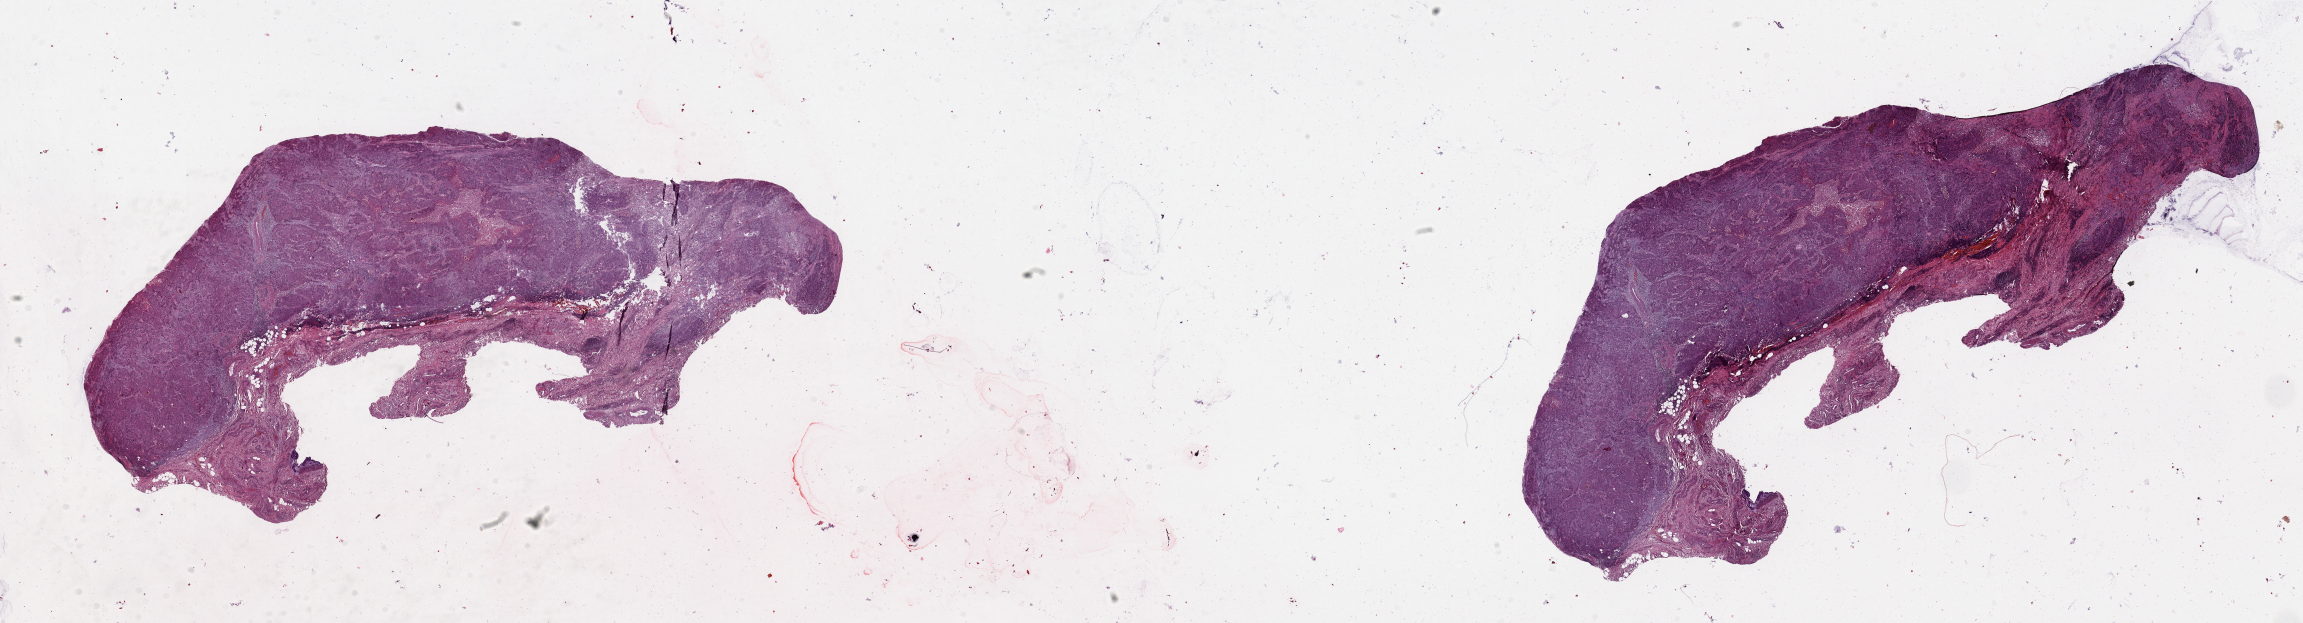
H&E whole-slide image — shown as a low-resolution overview of the whole scanned area (about 36.4 x 9.9 mm). Tumour tissue sample, sampled site: lung. Male, 57 y/o. Histologic grade: G2 (moderately differentiated). Composition of this section per pathologist review: tumour nuclei 70%, necrosis 5%.
Diagnosis: Squamous cell carcinoma, NOS. AJCC pathologic stage: IIA. Primary tumour site (as recorded): left upper lobe.